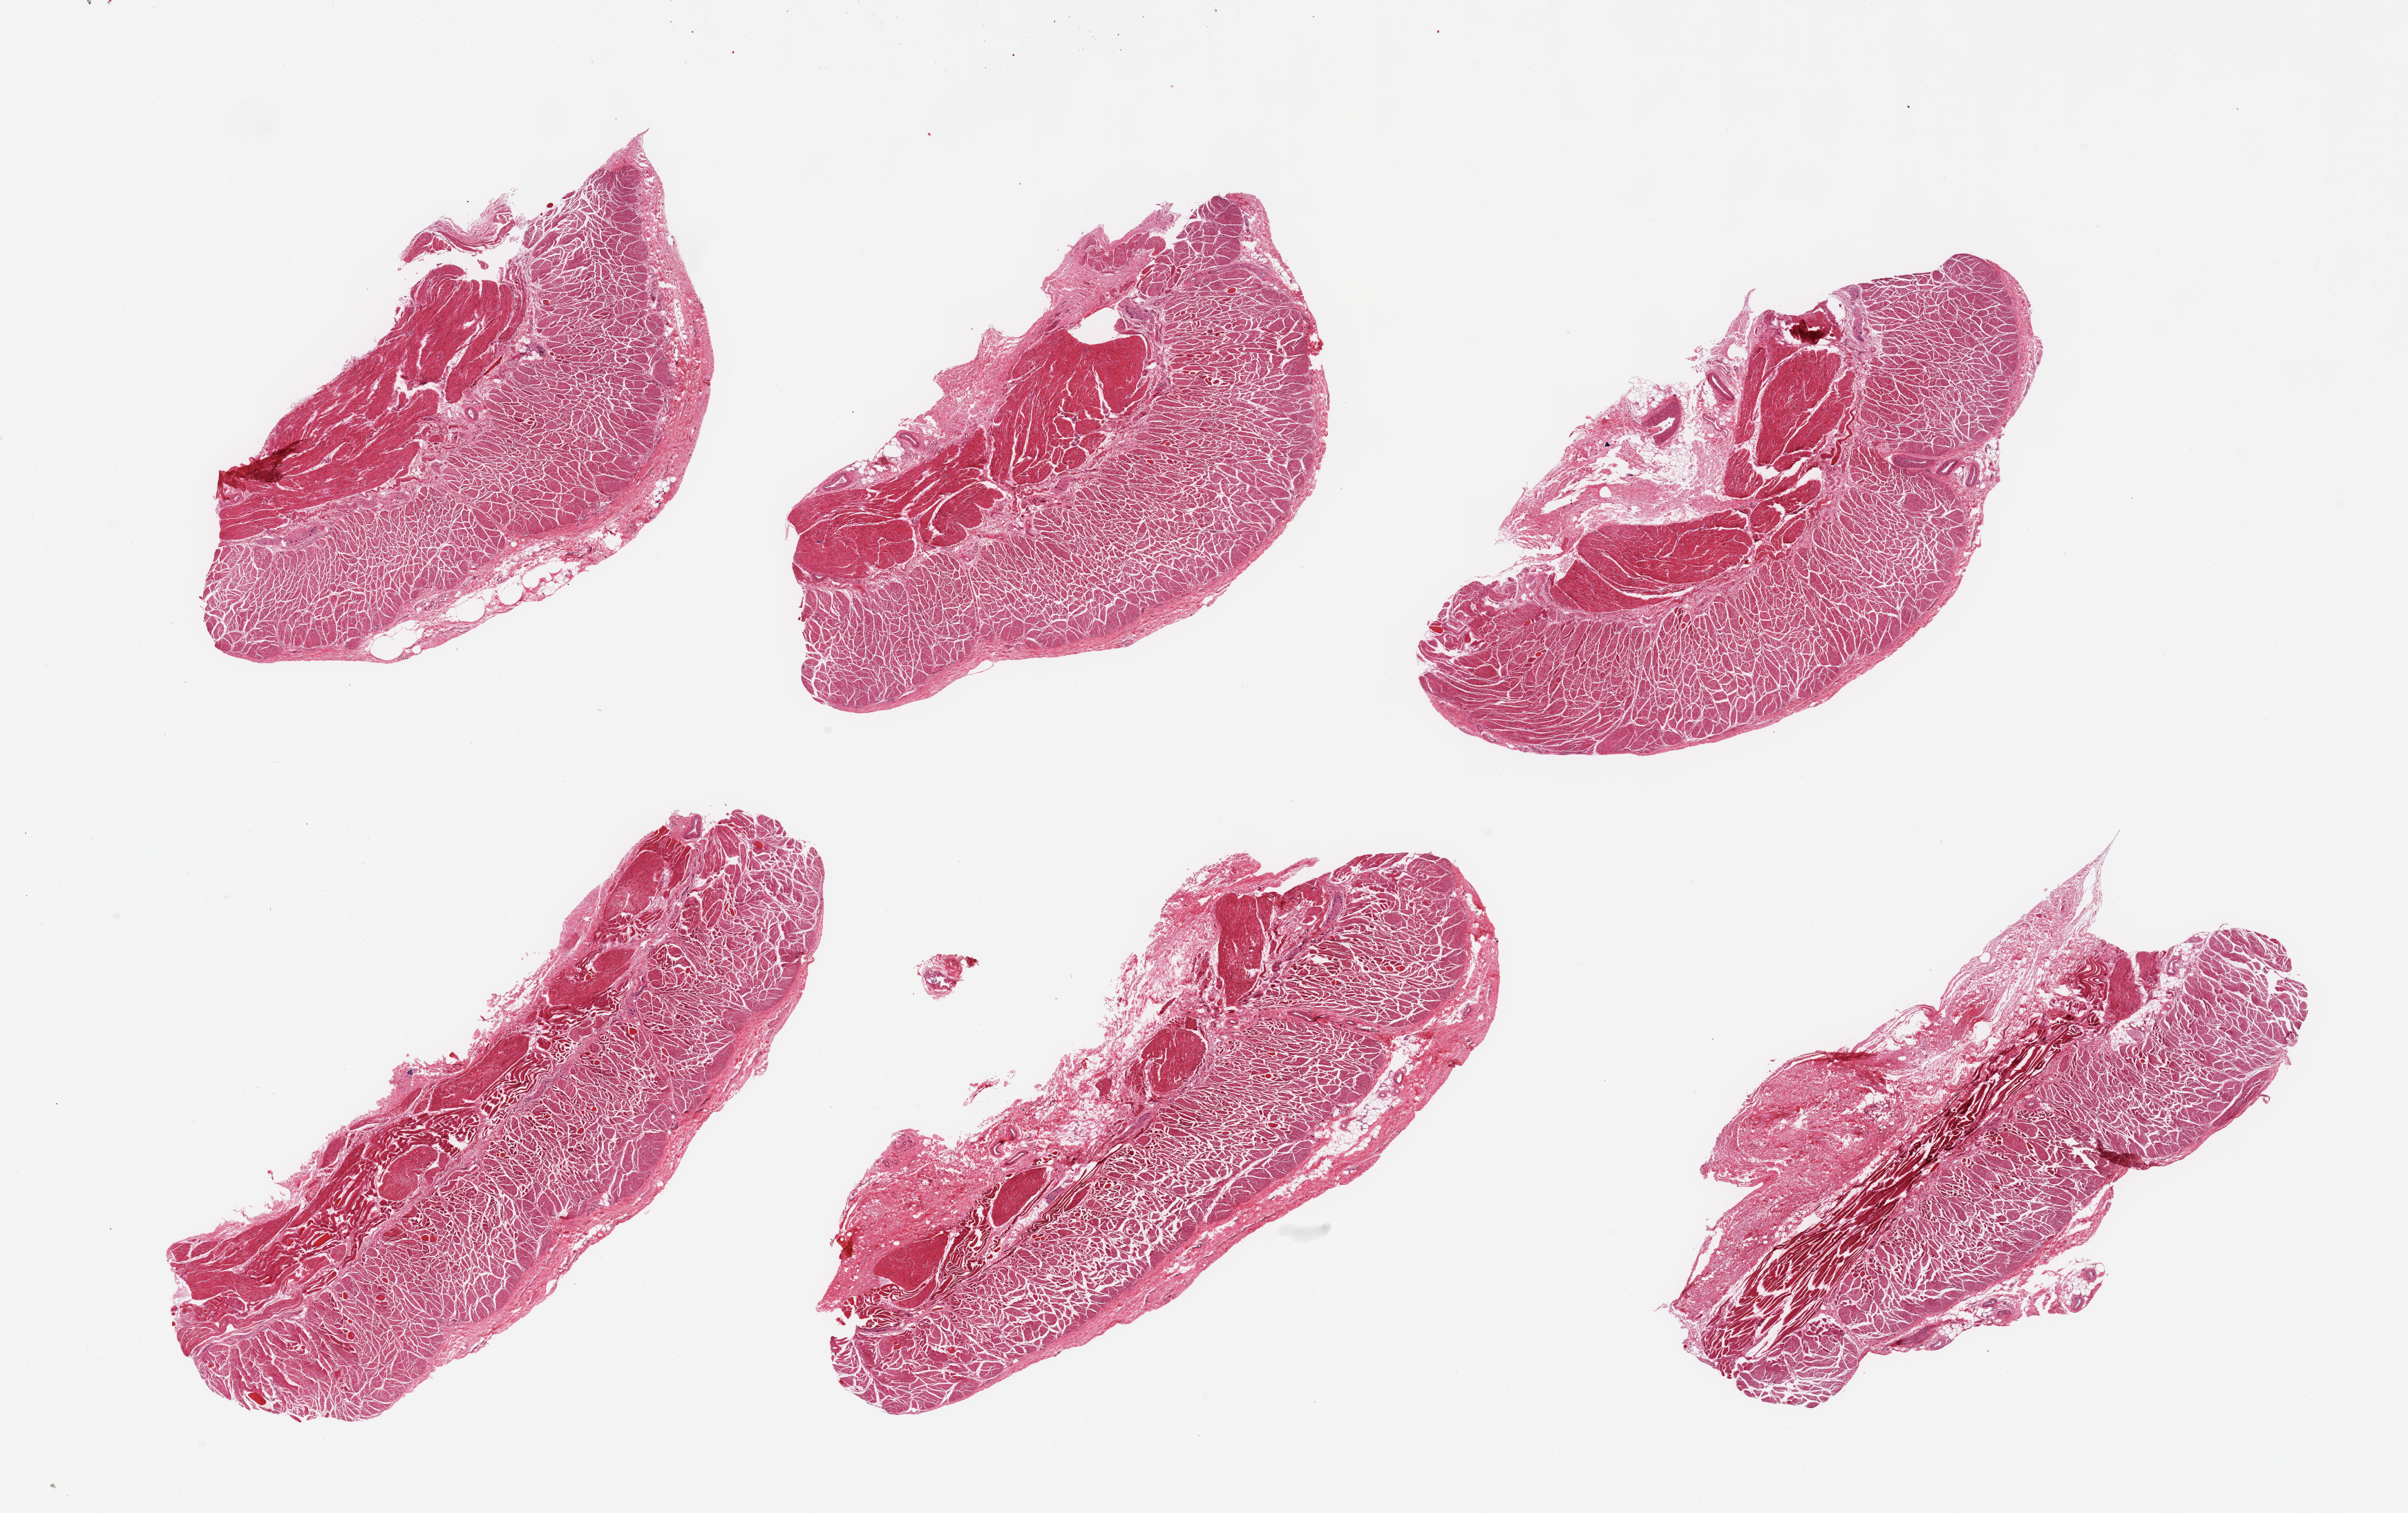
Whole-slide image, H&E stain, brightfield, a low-resolution overview of the entire scanned area, about 27.6 x 17.3 mm, PAXgene-fixed paraffin-embedded (PFPE) section, section of esophageal muscle (target tissue), donor tissue sample. Donor: male.
Pathologist's review note for this sample: 6 pieces; 20% admixture with skeletal muscle; up to 30% fibrovascular and fatty content in submucosal portion.